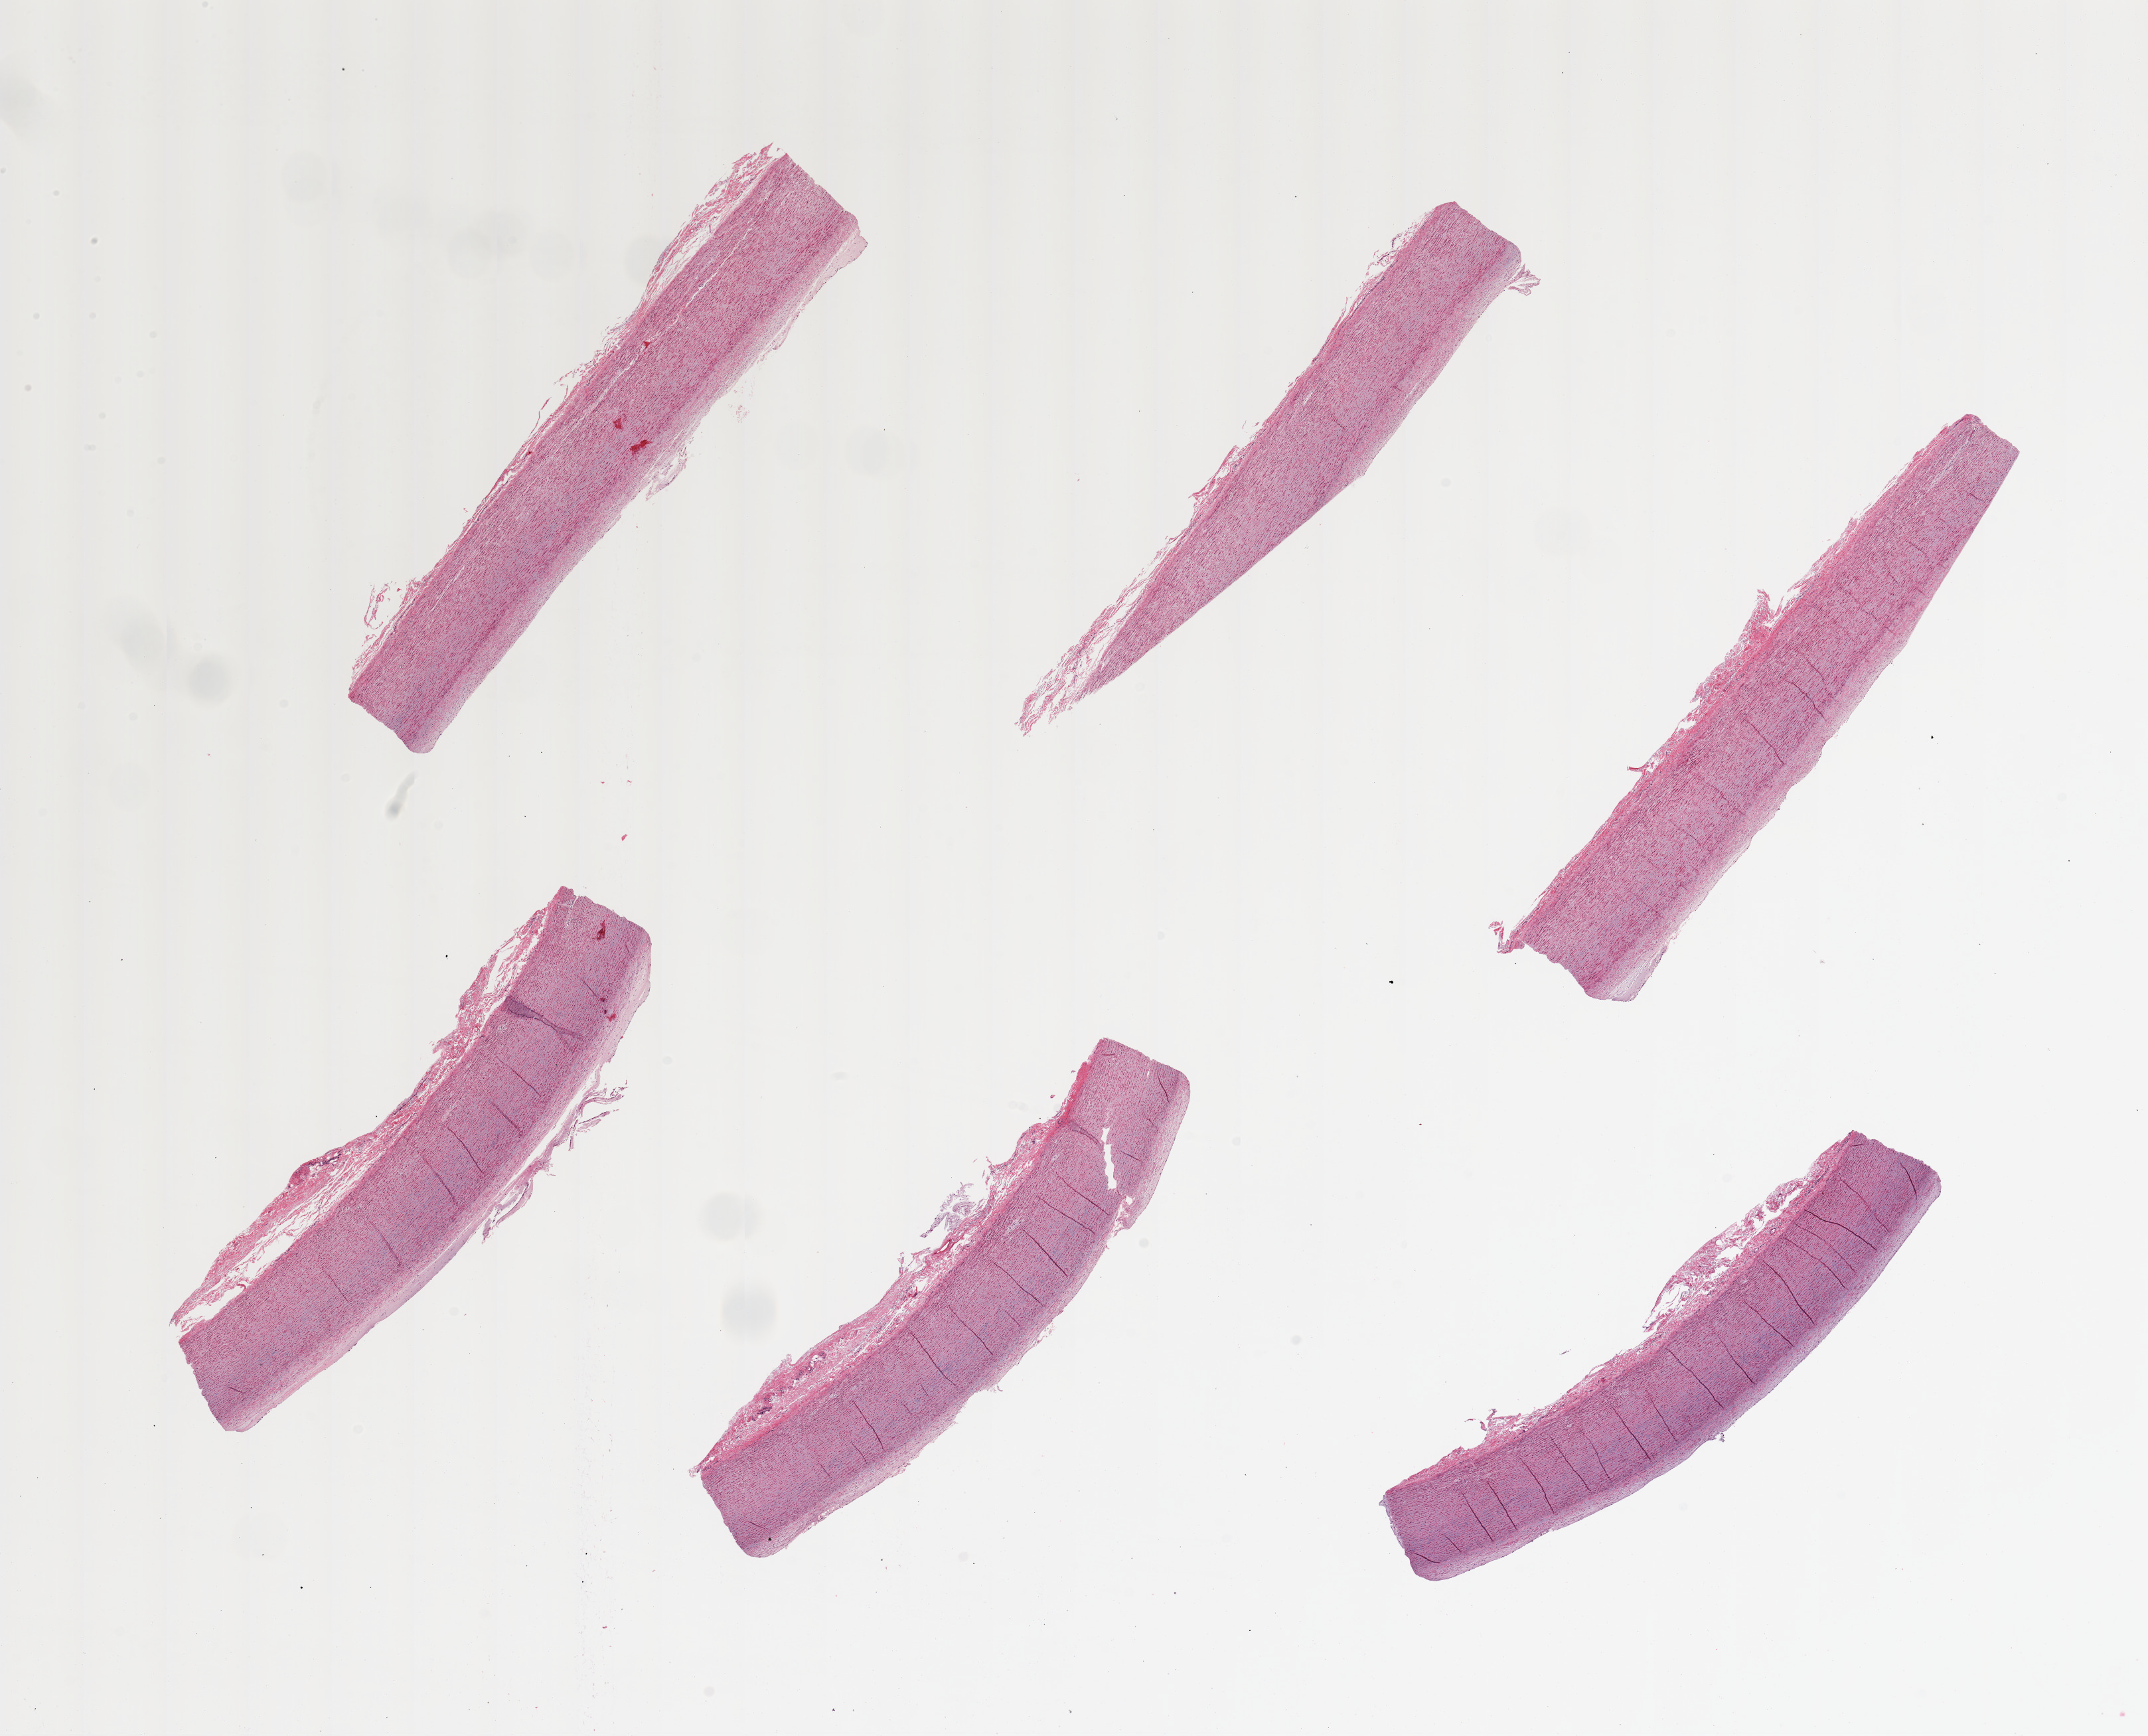
Whole-slide image, H&E stain, low-resolution overview of the scanned area, about 25.6 x 20.7 mm, PAXgene-fixed, paraffin-embedded tissue, sampled site (target tissue): aorta, donor tissue sample. Donor: female.
Reviewer comment on this tissue sample: 6 pieces, up to 8x2mm; well trimmed; minimal plaque.